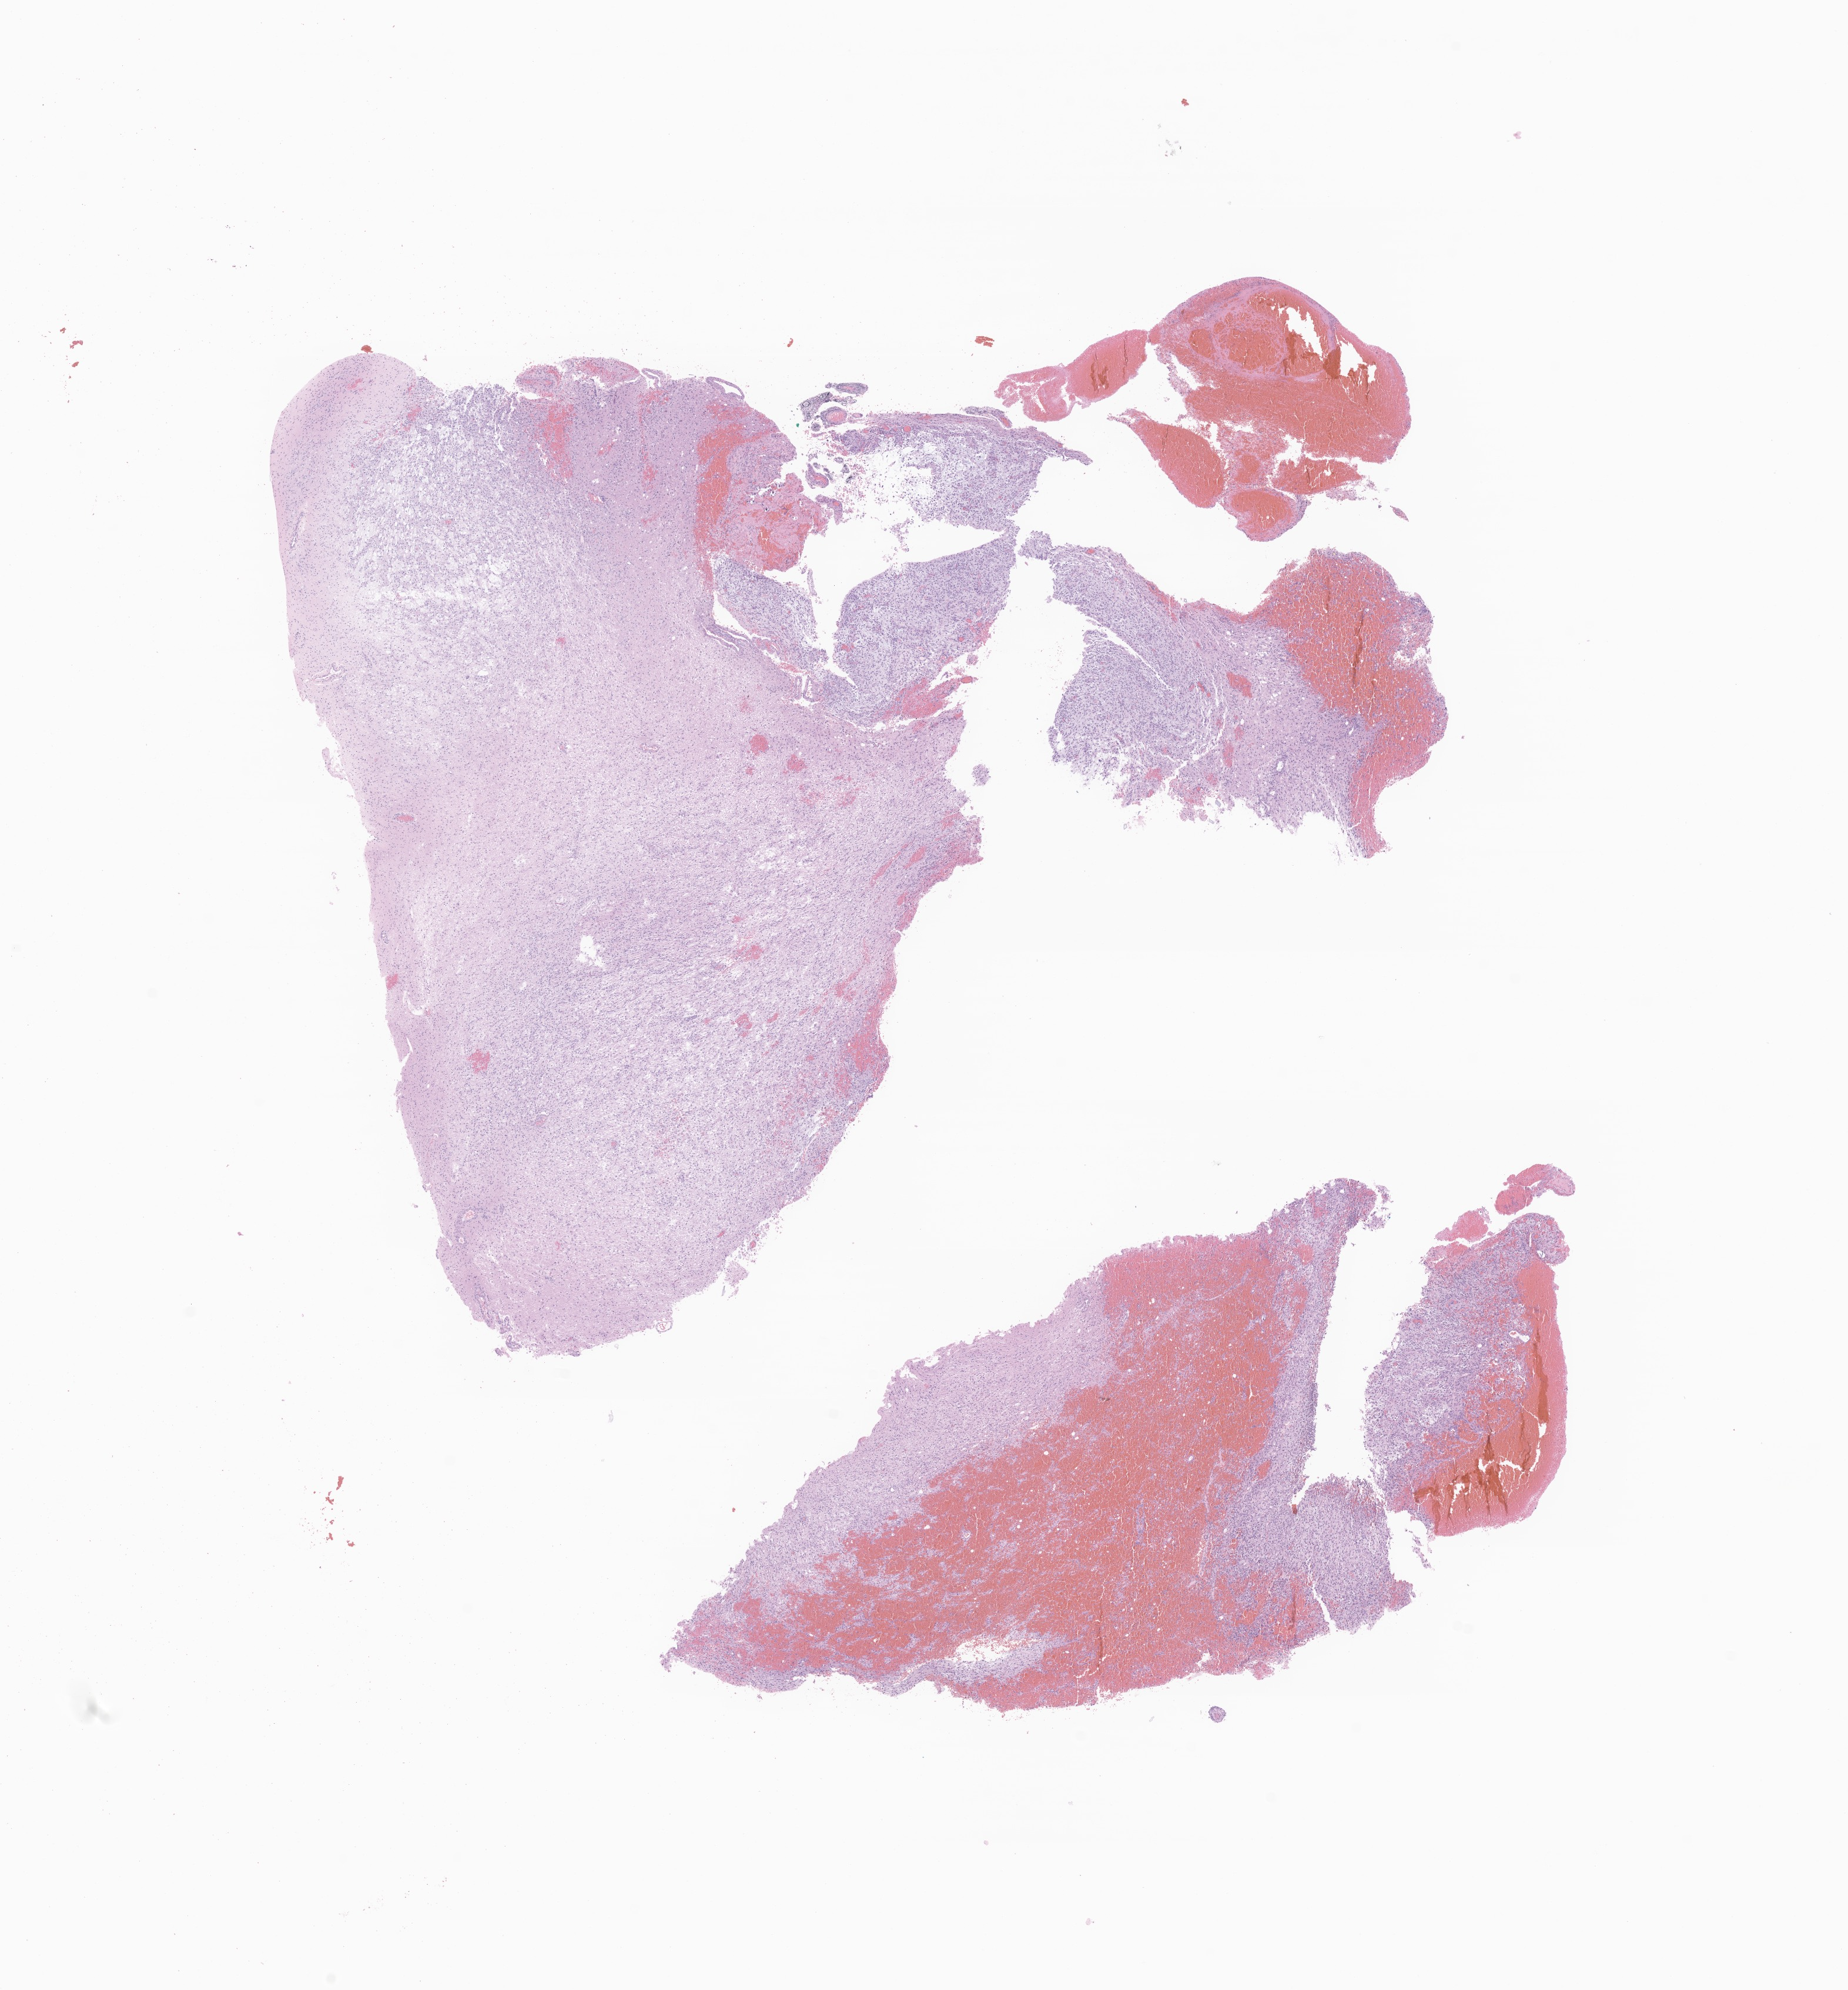
Digitized H&E-stained section of tumor tissue from the occipital lobe, low-resolution overview of the scanned area, about 13.3 x 14.3 mm. FFPE section. Patient: male, age 204 months (17 years).
Diagnosis (ICD-O-3 morphology term): Neoplasm, uncertain whether benign or malignant.